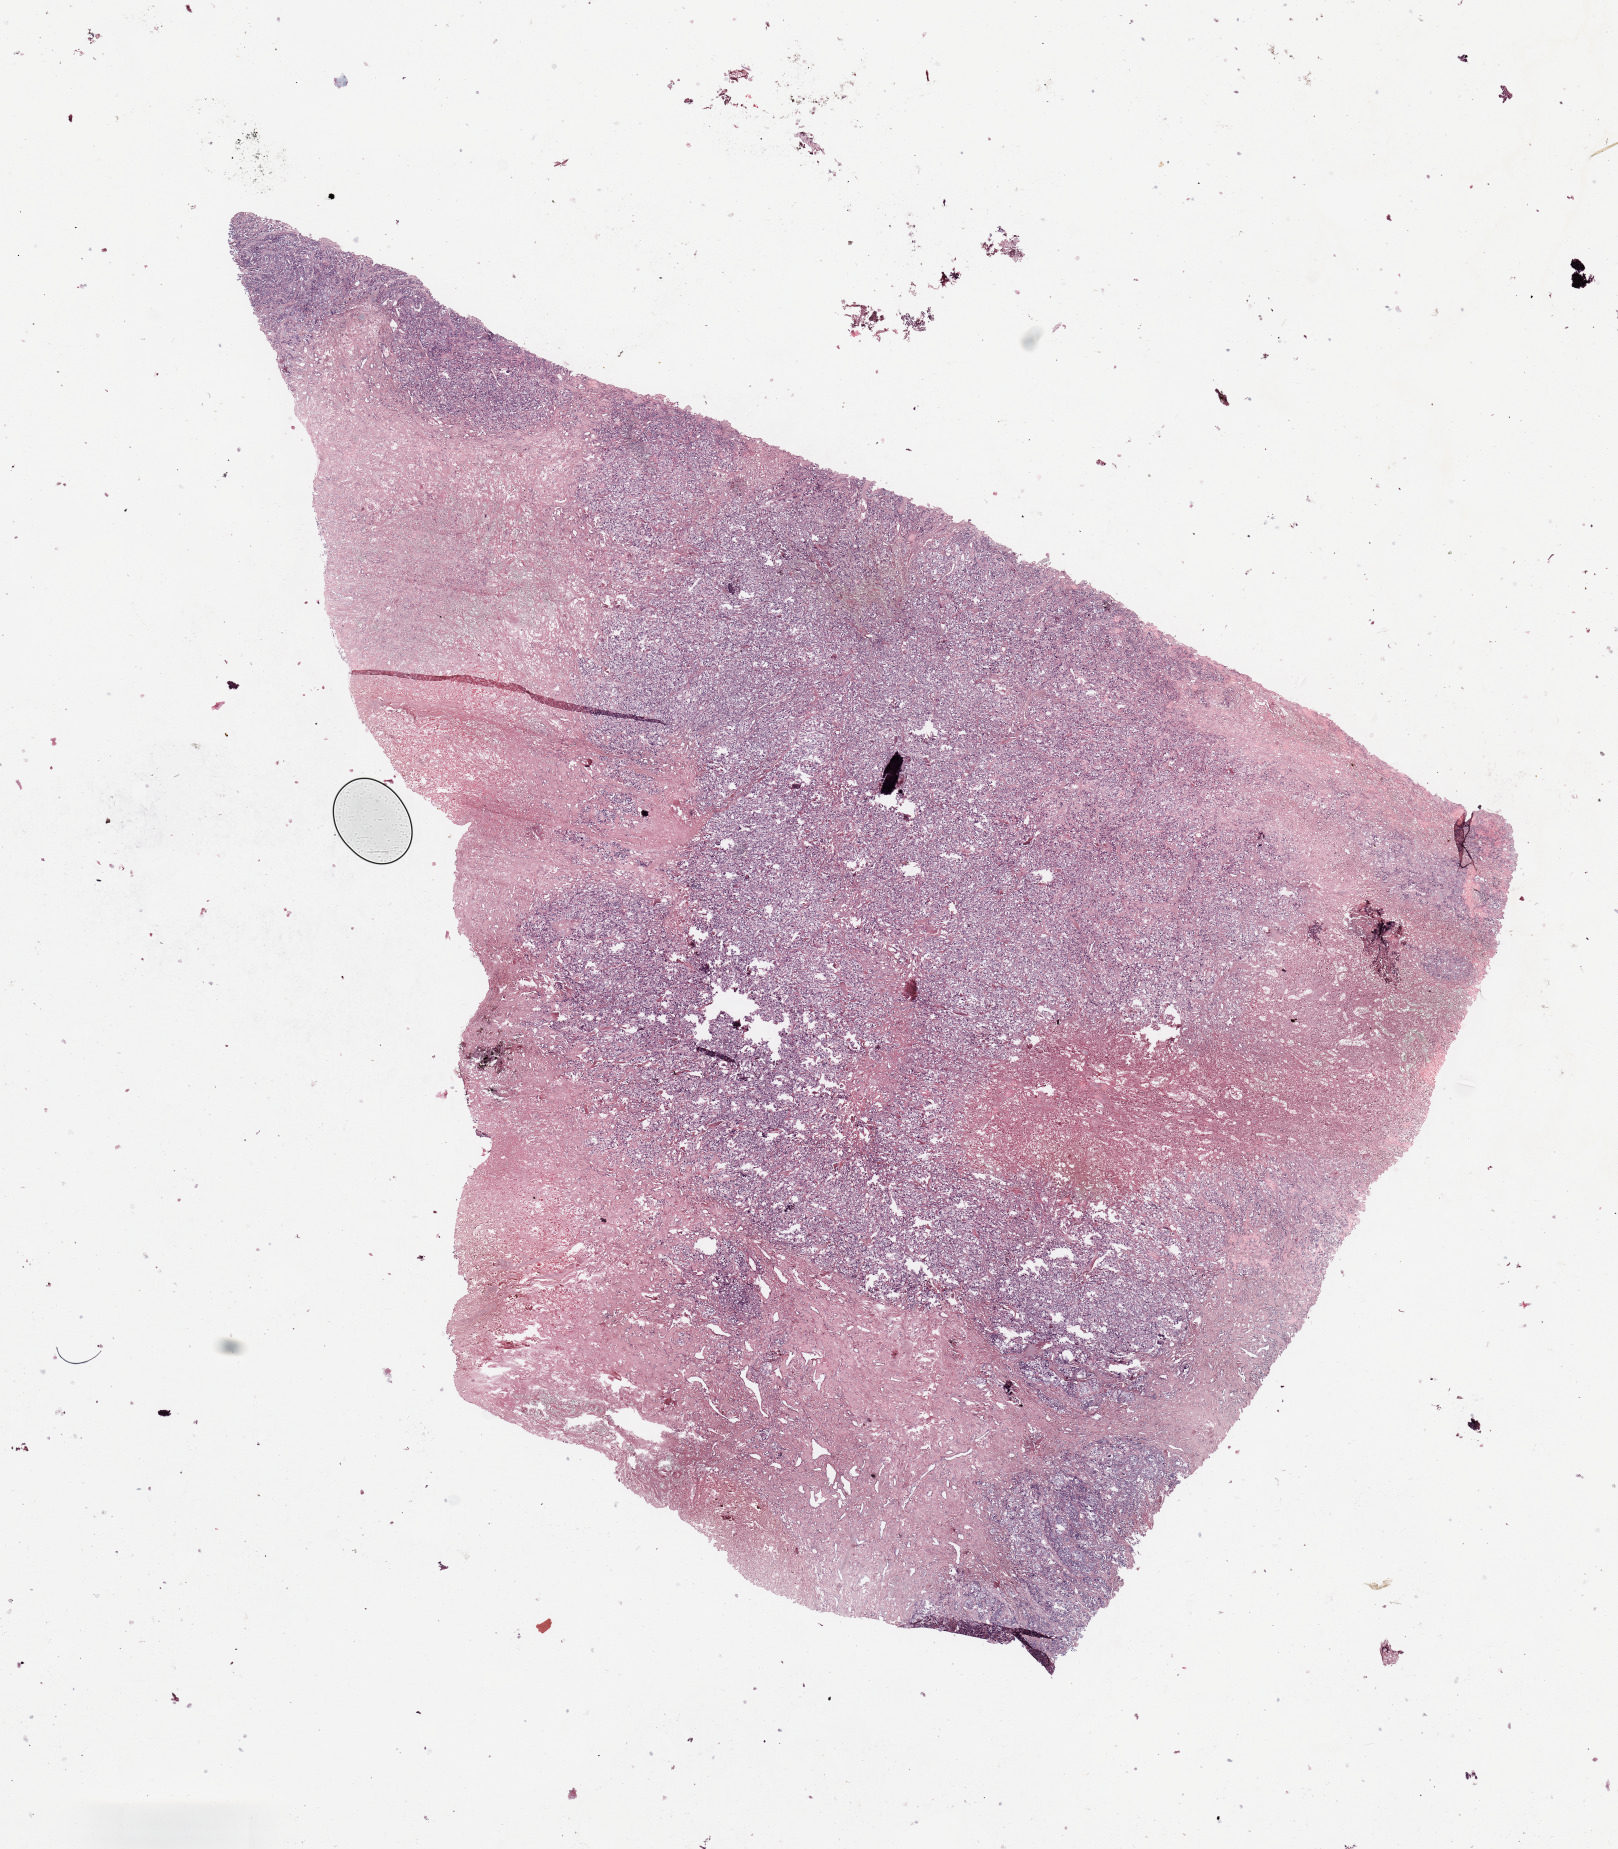
H&E whole-slide image — whole scanned area (about 12.8 x 14.6 mm, slide scanned at 20x) shown as a low-resolution overview, melanoma tumour tissue; sampled site not recorded. Female, 80 y/o.
Primary tumour site (as recorded): trunk. AJCC pathologic stage: IIA. Histologic diagnosis: Malignant melanoma, NOS.